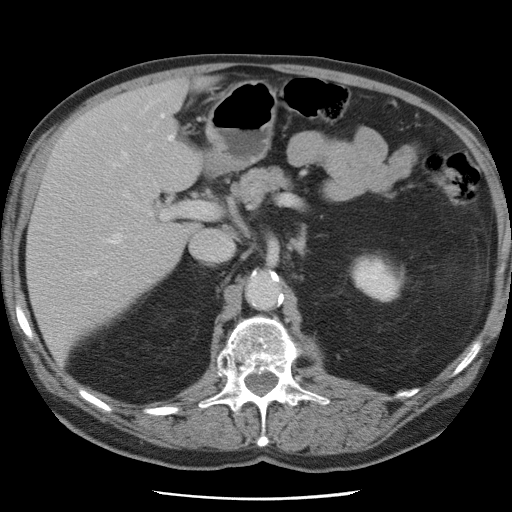
Contrast-enhanced abdominal CT, one axial slice; slice 43 of 78 in the series (ordered by position); intravenous contrast given; soft-tissue window (W 400 / L 40 HU); 5 mm slice thickness; 512 × 512 image matrix. Male patient, age 75 years. From the clinical record (not read from this slice): diagnosis: colorectal cancer liver metastases, imaged before liver resection; multiple liver metastases: yes; largest metastasis: 2.4 cm; chemotherapy before resection: yes.
Outlined on this slice (outlined manually by an expert reader):
- hepatic veins: bounding box (x1, y1, x2, y2) in pixels: (83, 127, 150, 280)
- liver: (29, 81, 200, 356)
- planned liver remnant (the part of the liver to remain after resection): (28, 120, 188, 356)
- portal vein (with intrahepatic branches): (123, 136, 196, 219)